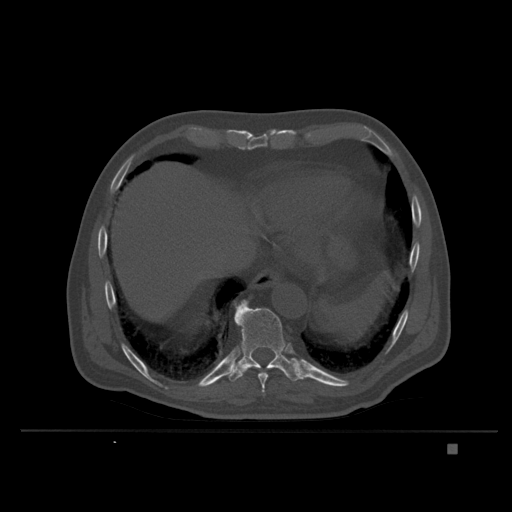
CT including the spine, one axial slice. Slice 200 of 435 in the series (ordered by position). Bone window (W 1800 / L 400 HU). 1.5 mm slice thickness. 512 × 512 image matrix. Male patient, age 73 years. From the clinical record (not read from this slice): primary cancer: skin.
Structures marked on this image (semi-automatically segmented with operator editing):
- T10 vertebra: bounding box <226,300,304,382> (left, top, right, bottom; pixels)
- T9 vertebra: <236,300,271,396>